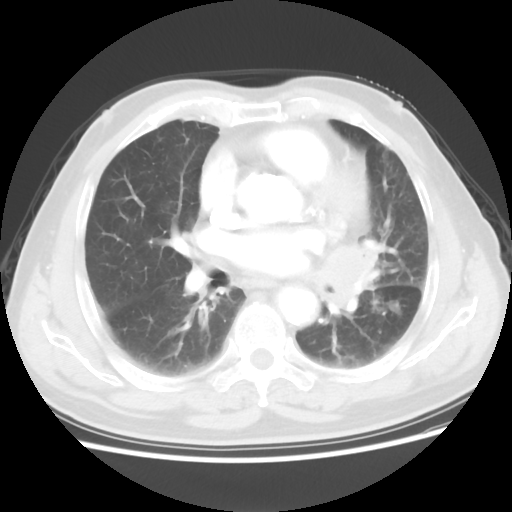
Chest CT, one axial slice; position 30 of 56 along the scan axis; 120 kVp; lung window (W 1500 / L -600 HU); 512 × 512 image matrix. Male patient, age 75 years. Case-level facts recorded for this patient, not image findings: clinical TNM (as recorded): T3 N0 M0.
Outlined on this slice (rectangle marked by the reading radiologist):
- lung tumour (recorded histology: squamous cell carcinoma): box from (x=316, y=233) to (x=384, y=315) px